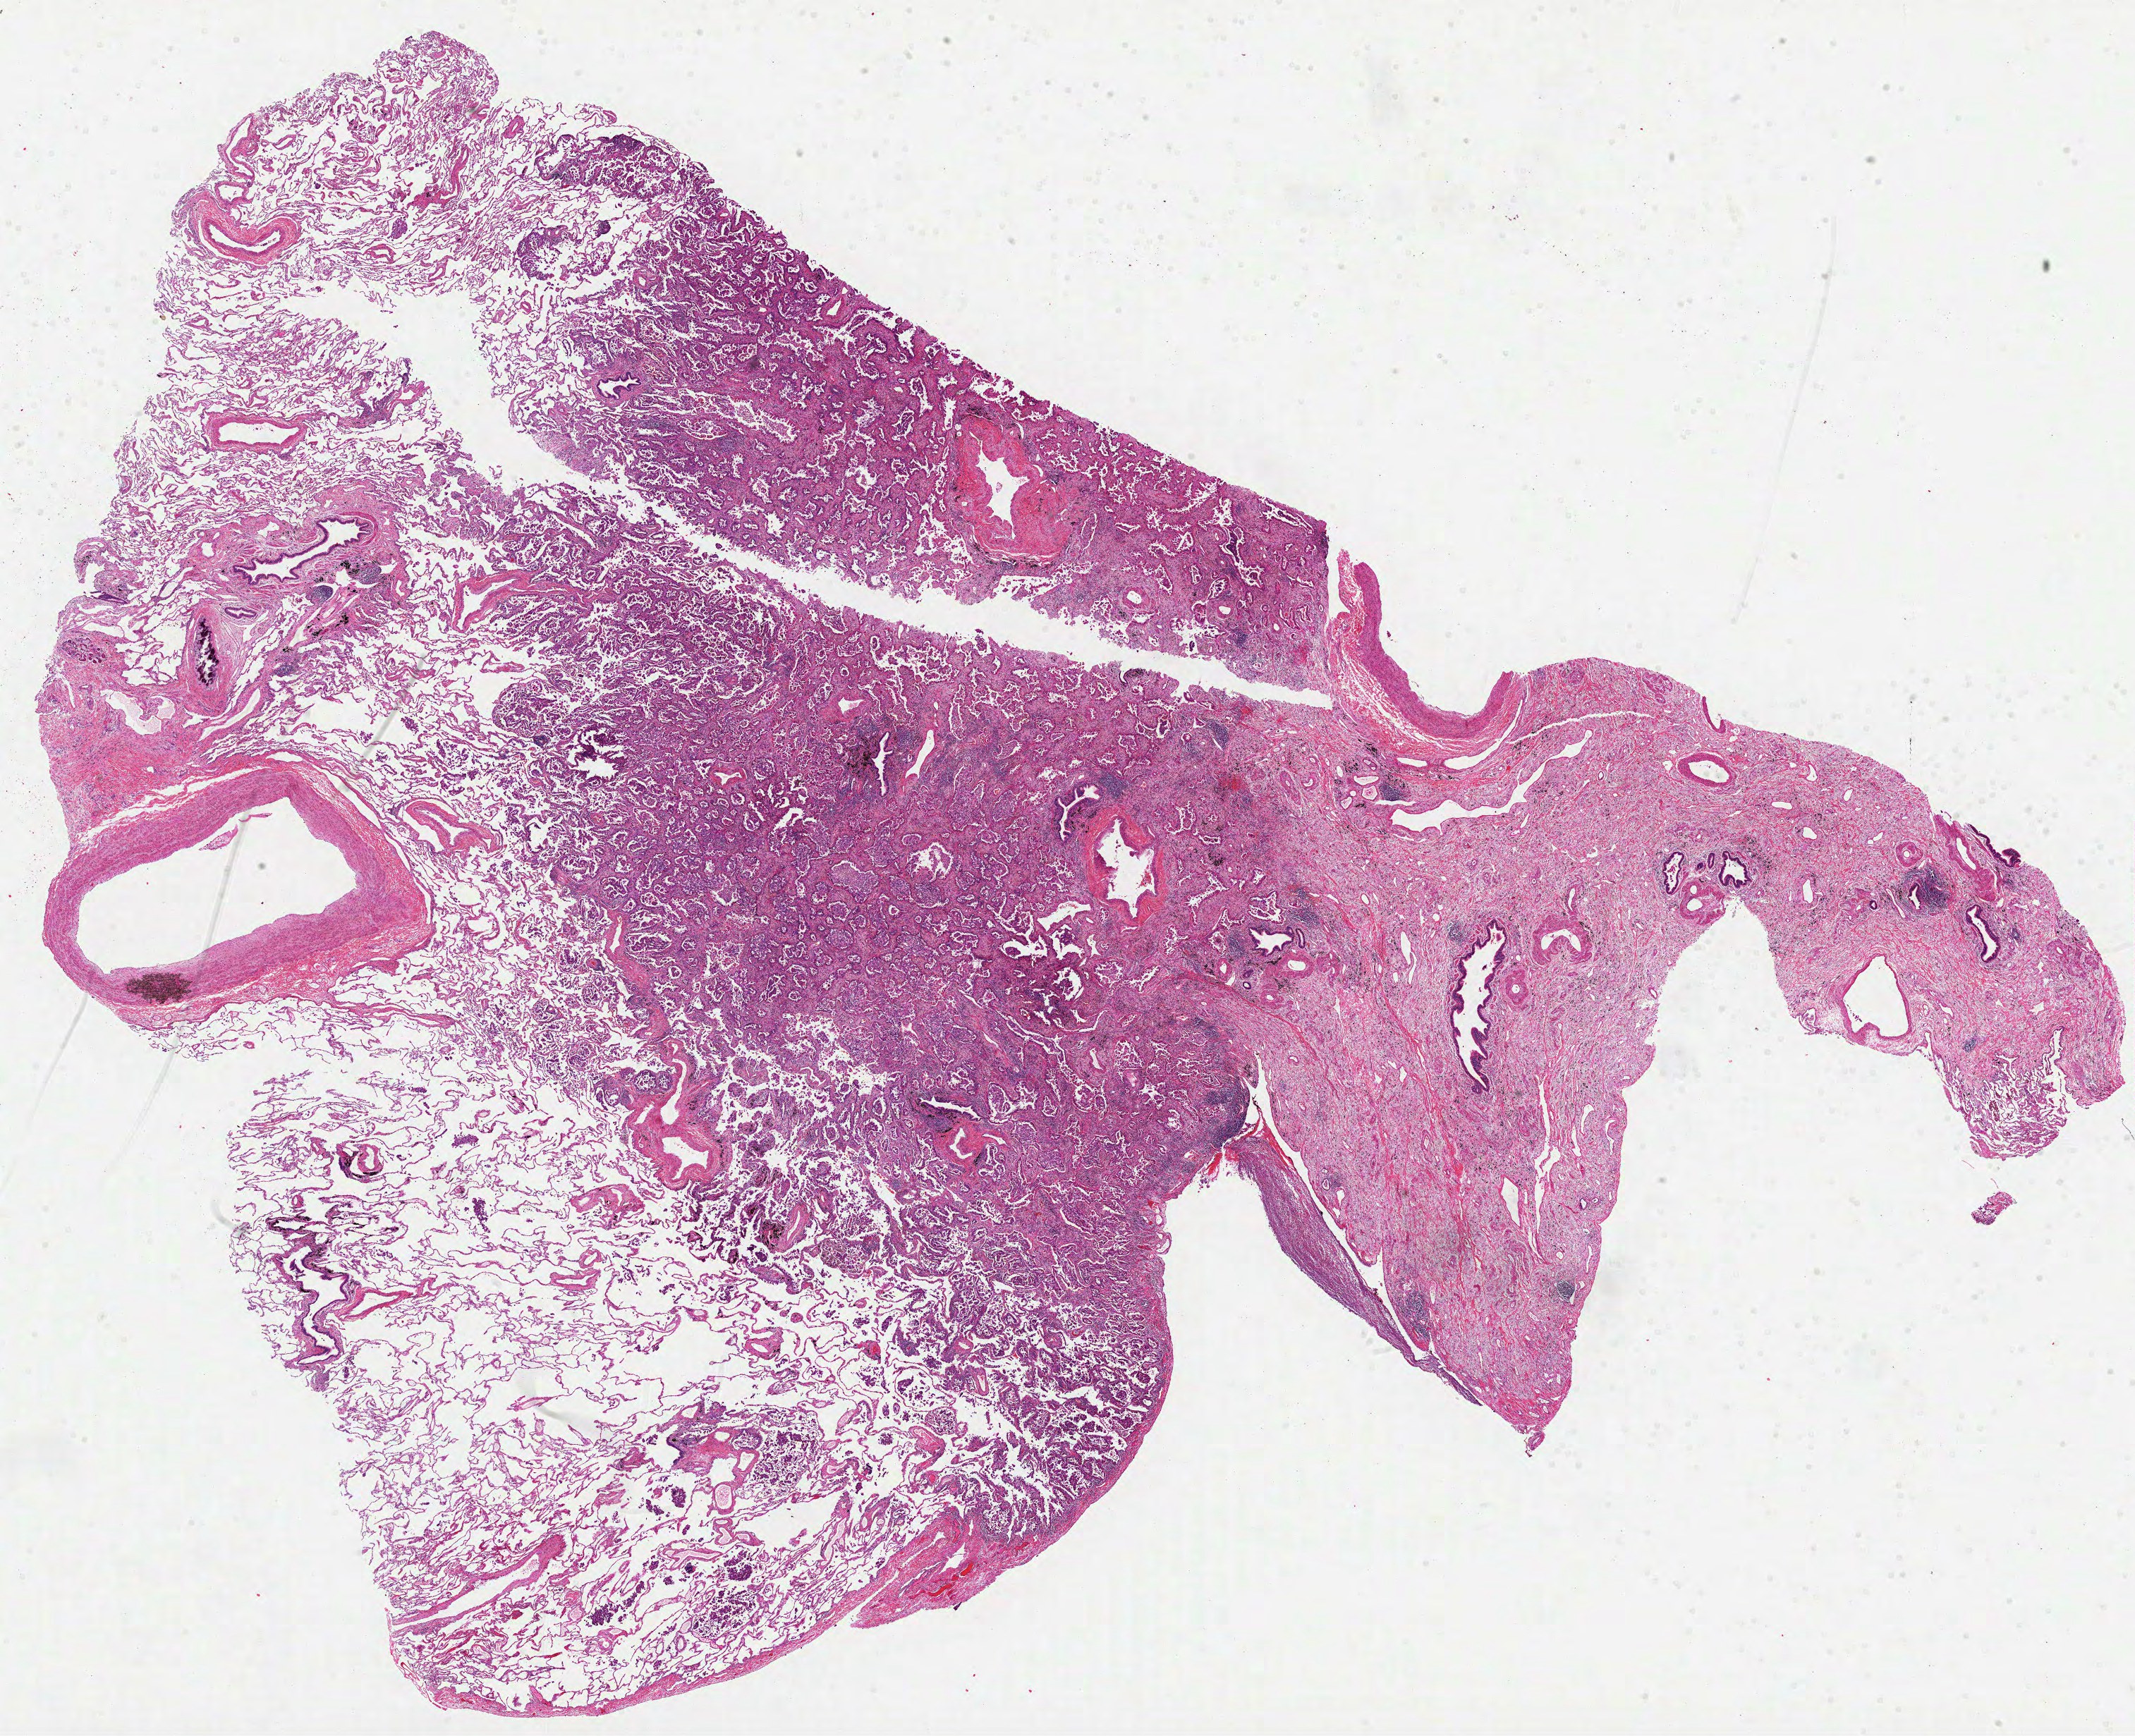
Digitized H&E tissue section (whole slide) — low-resolution overview of the scanned area, about 24.4 x 19.9 mm; FFPE section; sample: primary tumour, lung. Female, age 61 years at initial diagnosis.
AJCC pathologic stage: IIB (4th edition). Diagnosis: Adenocarcinoma, NOS (lower lobe, lung).